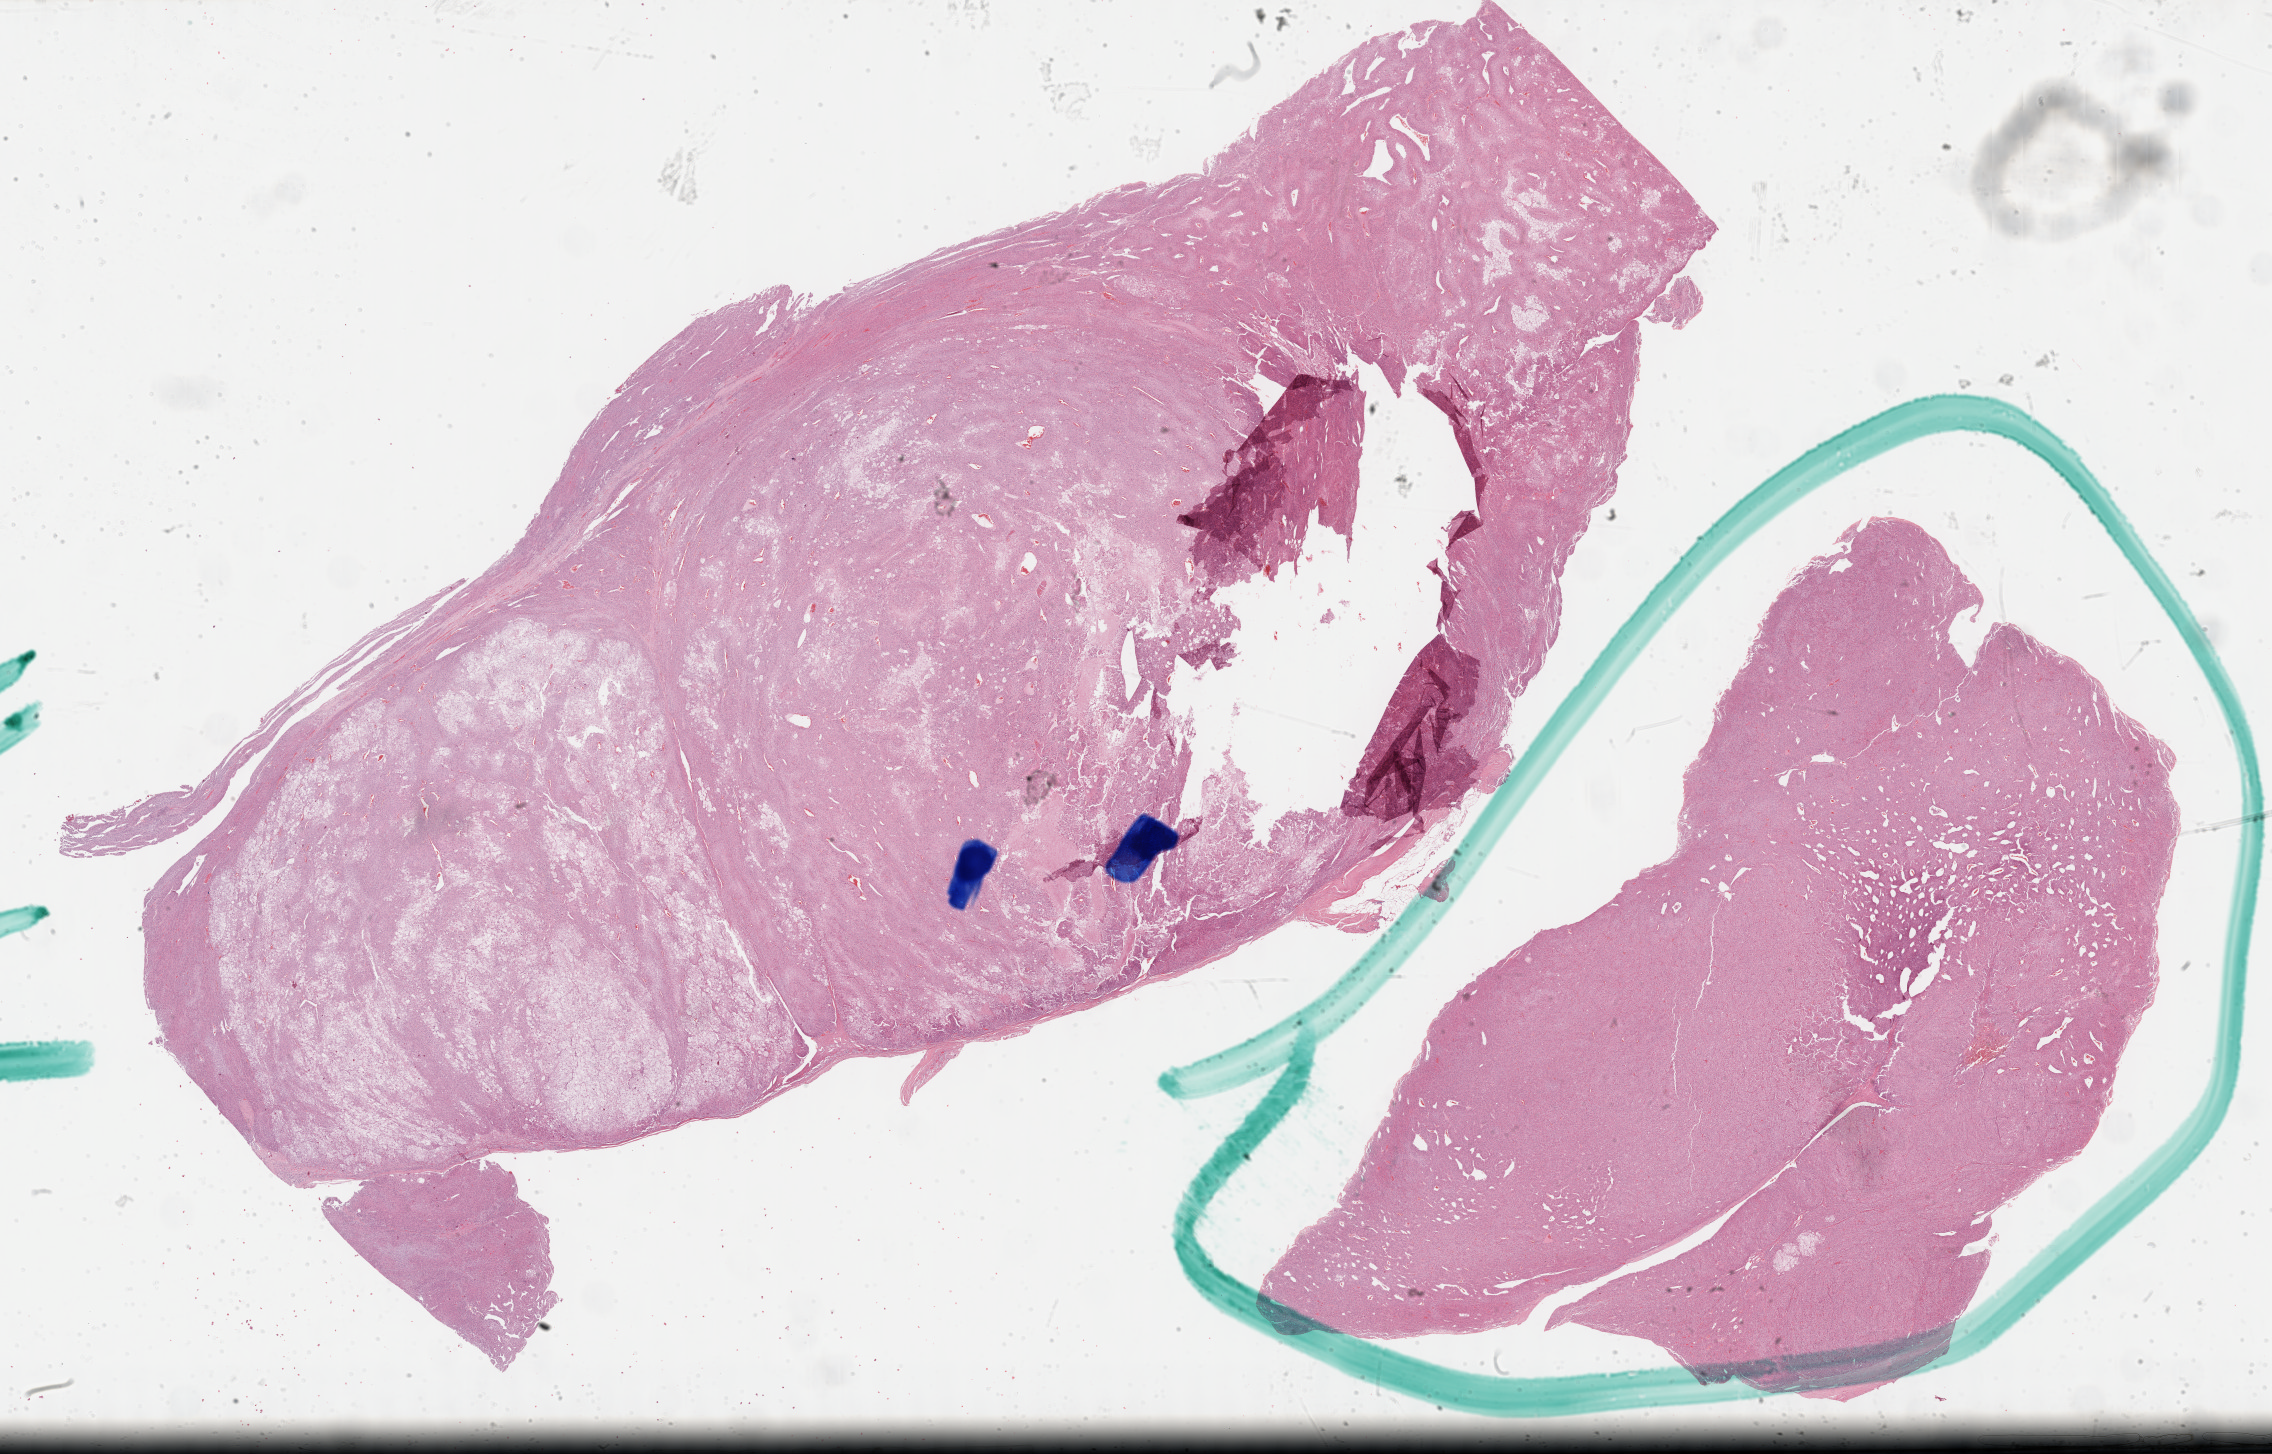
H&E-stained whole-slide image, whole scanned area (about 36.7 x 23.5 mm) shown as a low-resolution overview; formalin-fixed paraffin-embedded (FFPE) diagnostic section; sample: primary tumour, adrenal cortex. Patient: male, age at initial diagnosis 47 years.
* diagnosis: Adrenal cortical carcinoma (cortex of adrenal gland)
* laterality: right